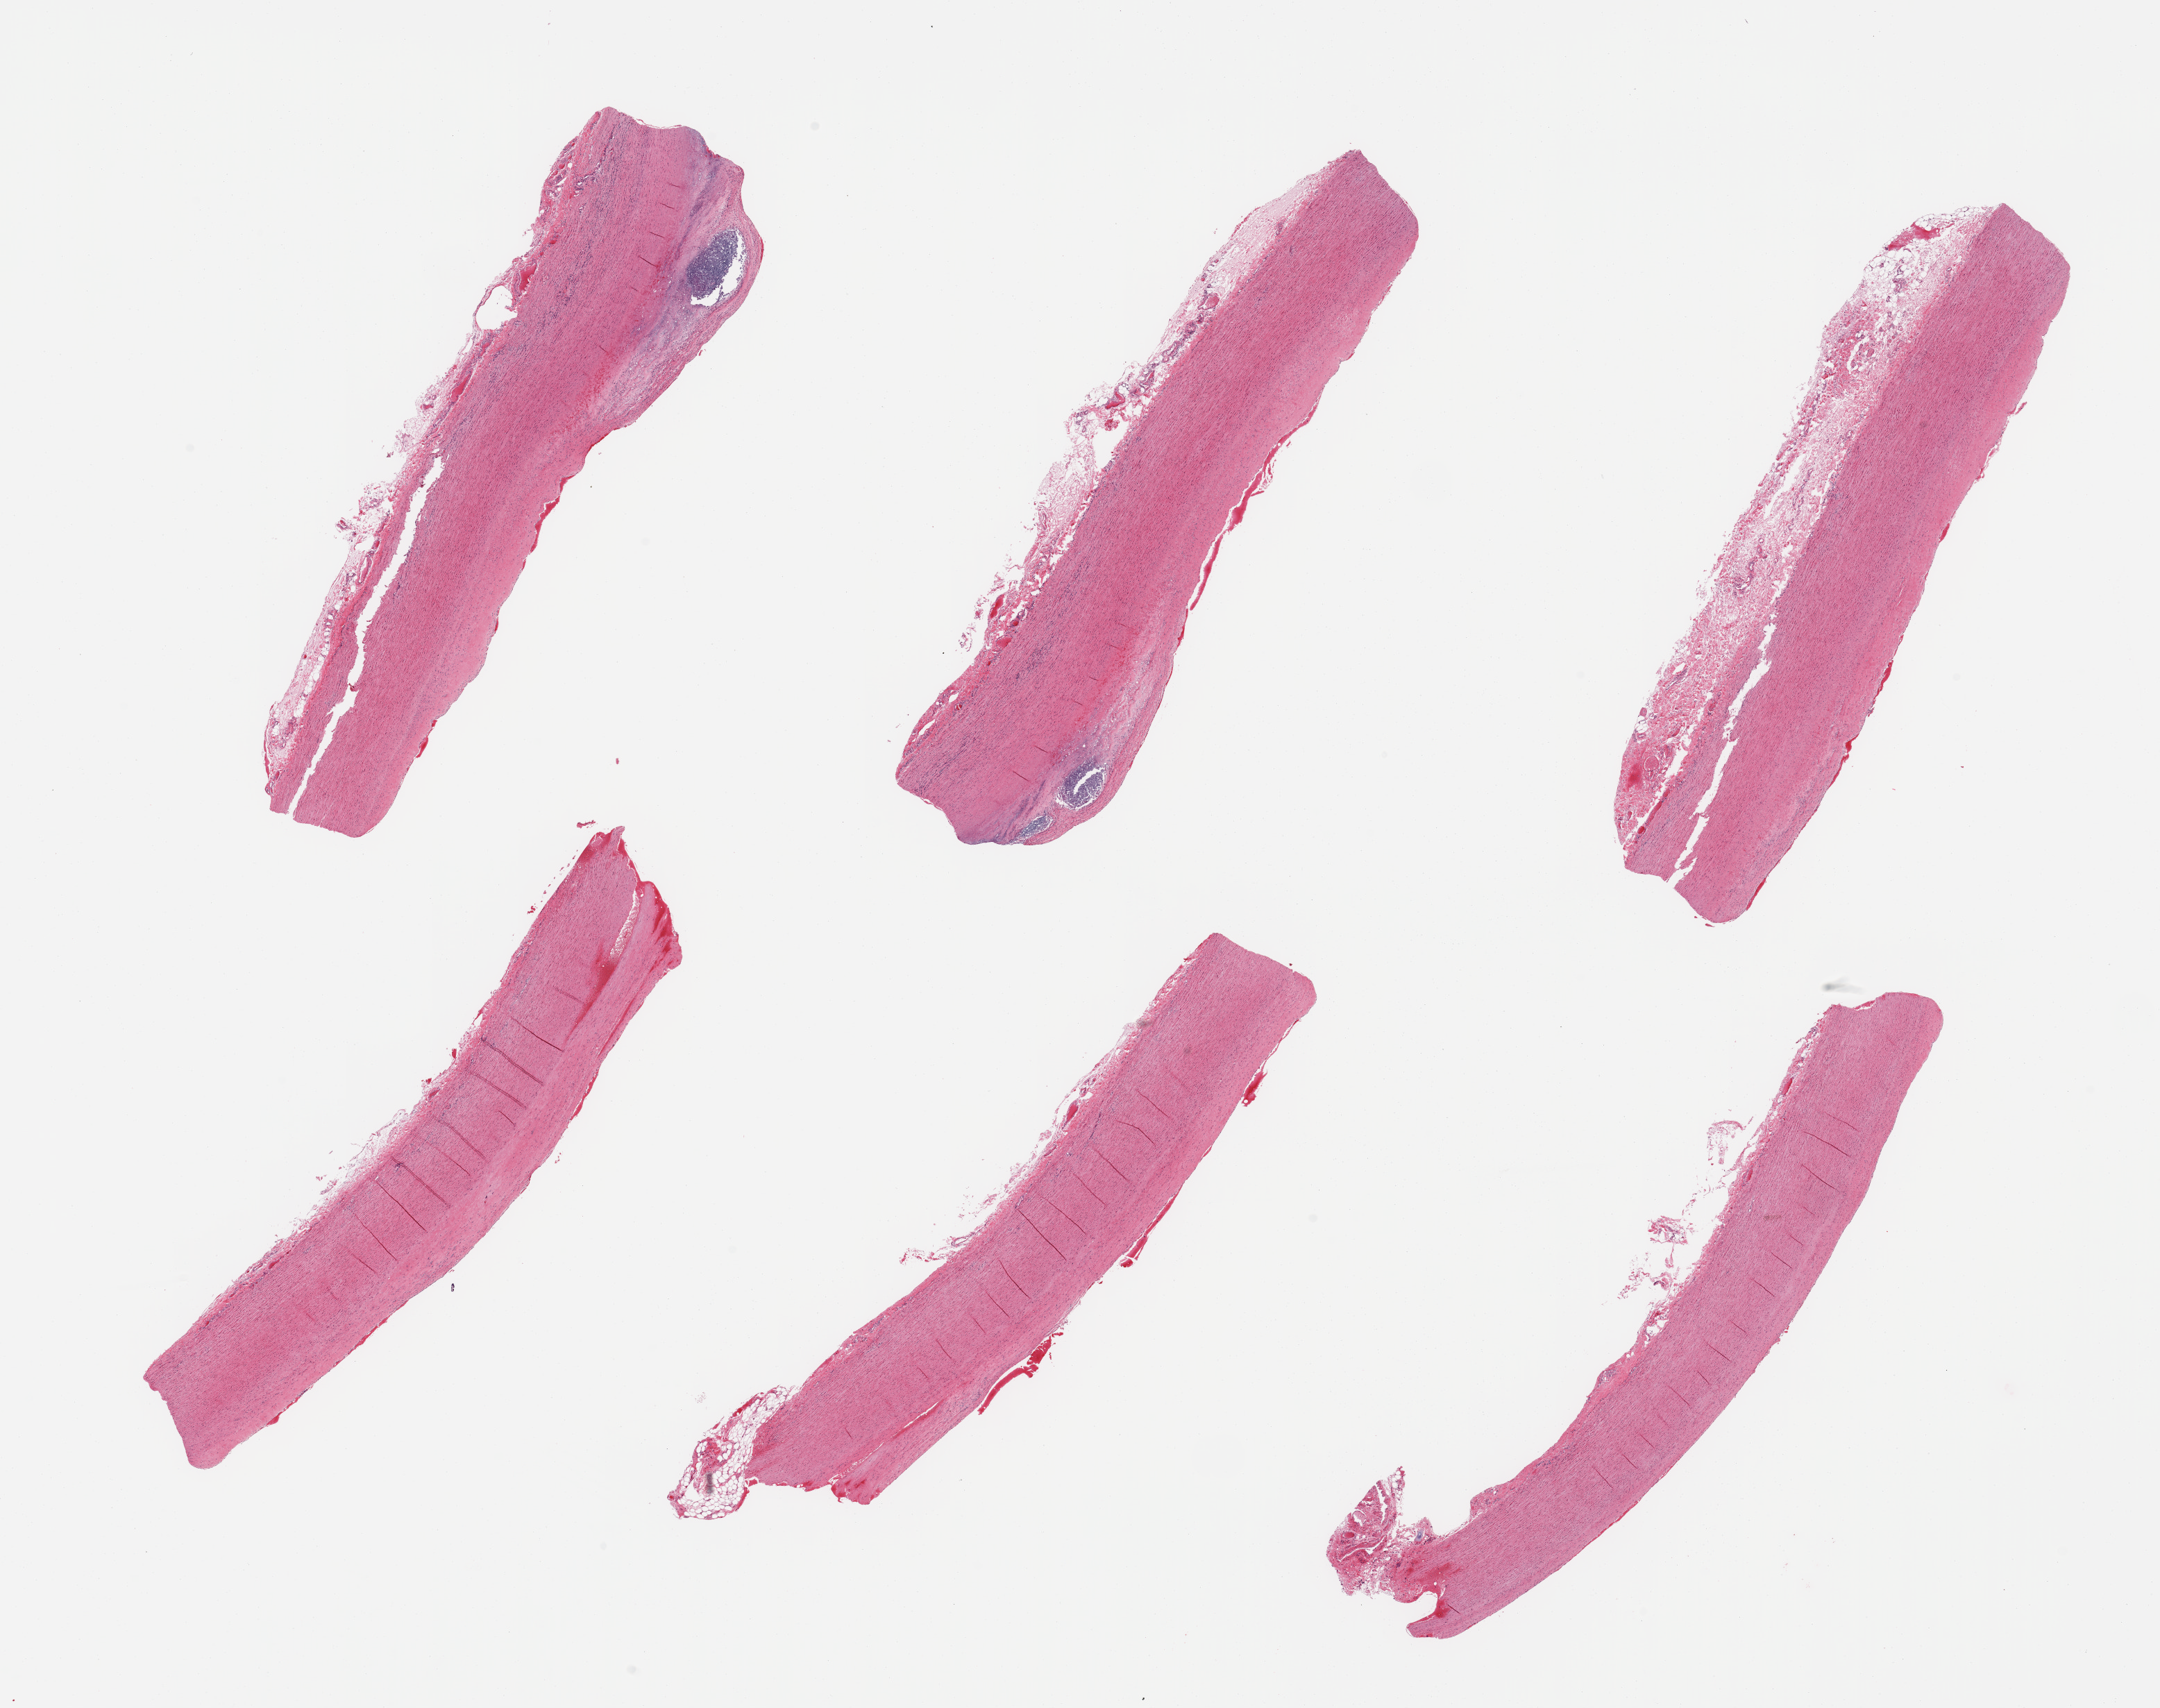
Haematoxylin and eosin whole-slide image, whole scanned area (about 24.6 x 19.5 mm) shown as a low-resolution overview; PAXgene-fixed paraffin-embedded (PFPE) section; target tissue: aorta; donor tissue sample. Male donor.
Review note (as recorded): 6 pieces, atherosis with inflammation, up to 1mm.